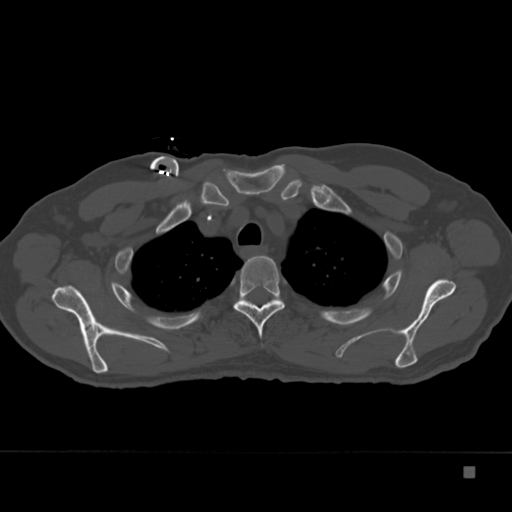
CT including the spine, one axial slice; position 286 of 332 along the scan axis; reconstruction kernel Br40s; 120 kVp; bone window (W 1800 / L 400 HU); 1.5 mm slice thickness; 512 × 512 image matrix, field of view 389 × 389 mm. Patient: male, 72 years. Case-level facts recorded for this patient, not image findings: primary cancer: skeletal.
Outlined on this slice (semi-automatic segmentation, software-assisted and operator-edited):
- T3 vertebra: bounding box (x1, y1, x2, y2) in pixels: (234, 256, 285, 346)